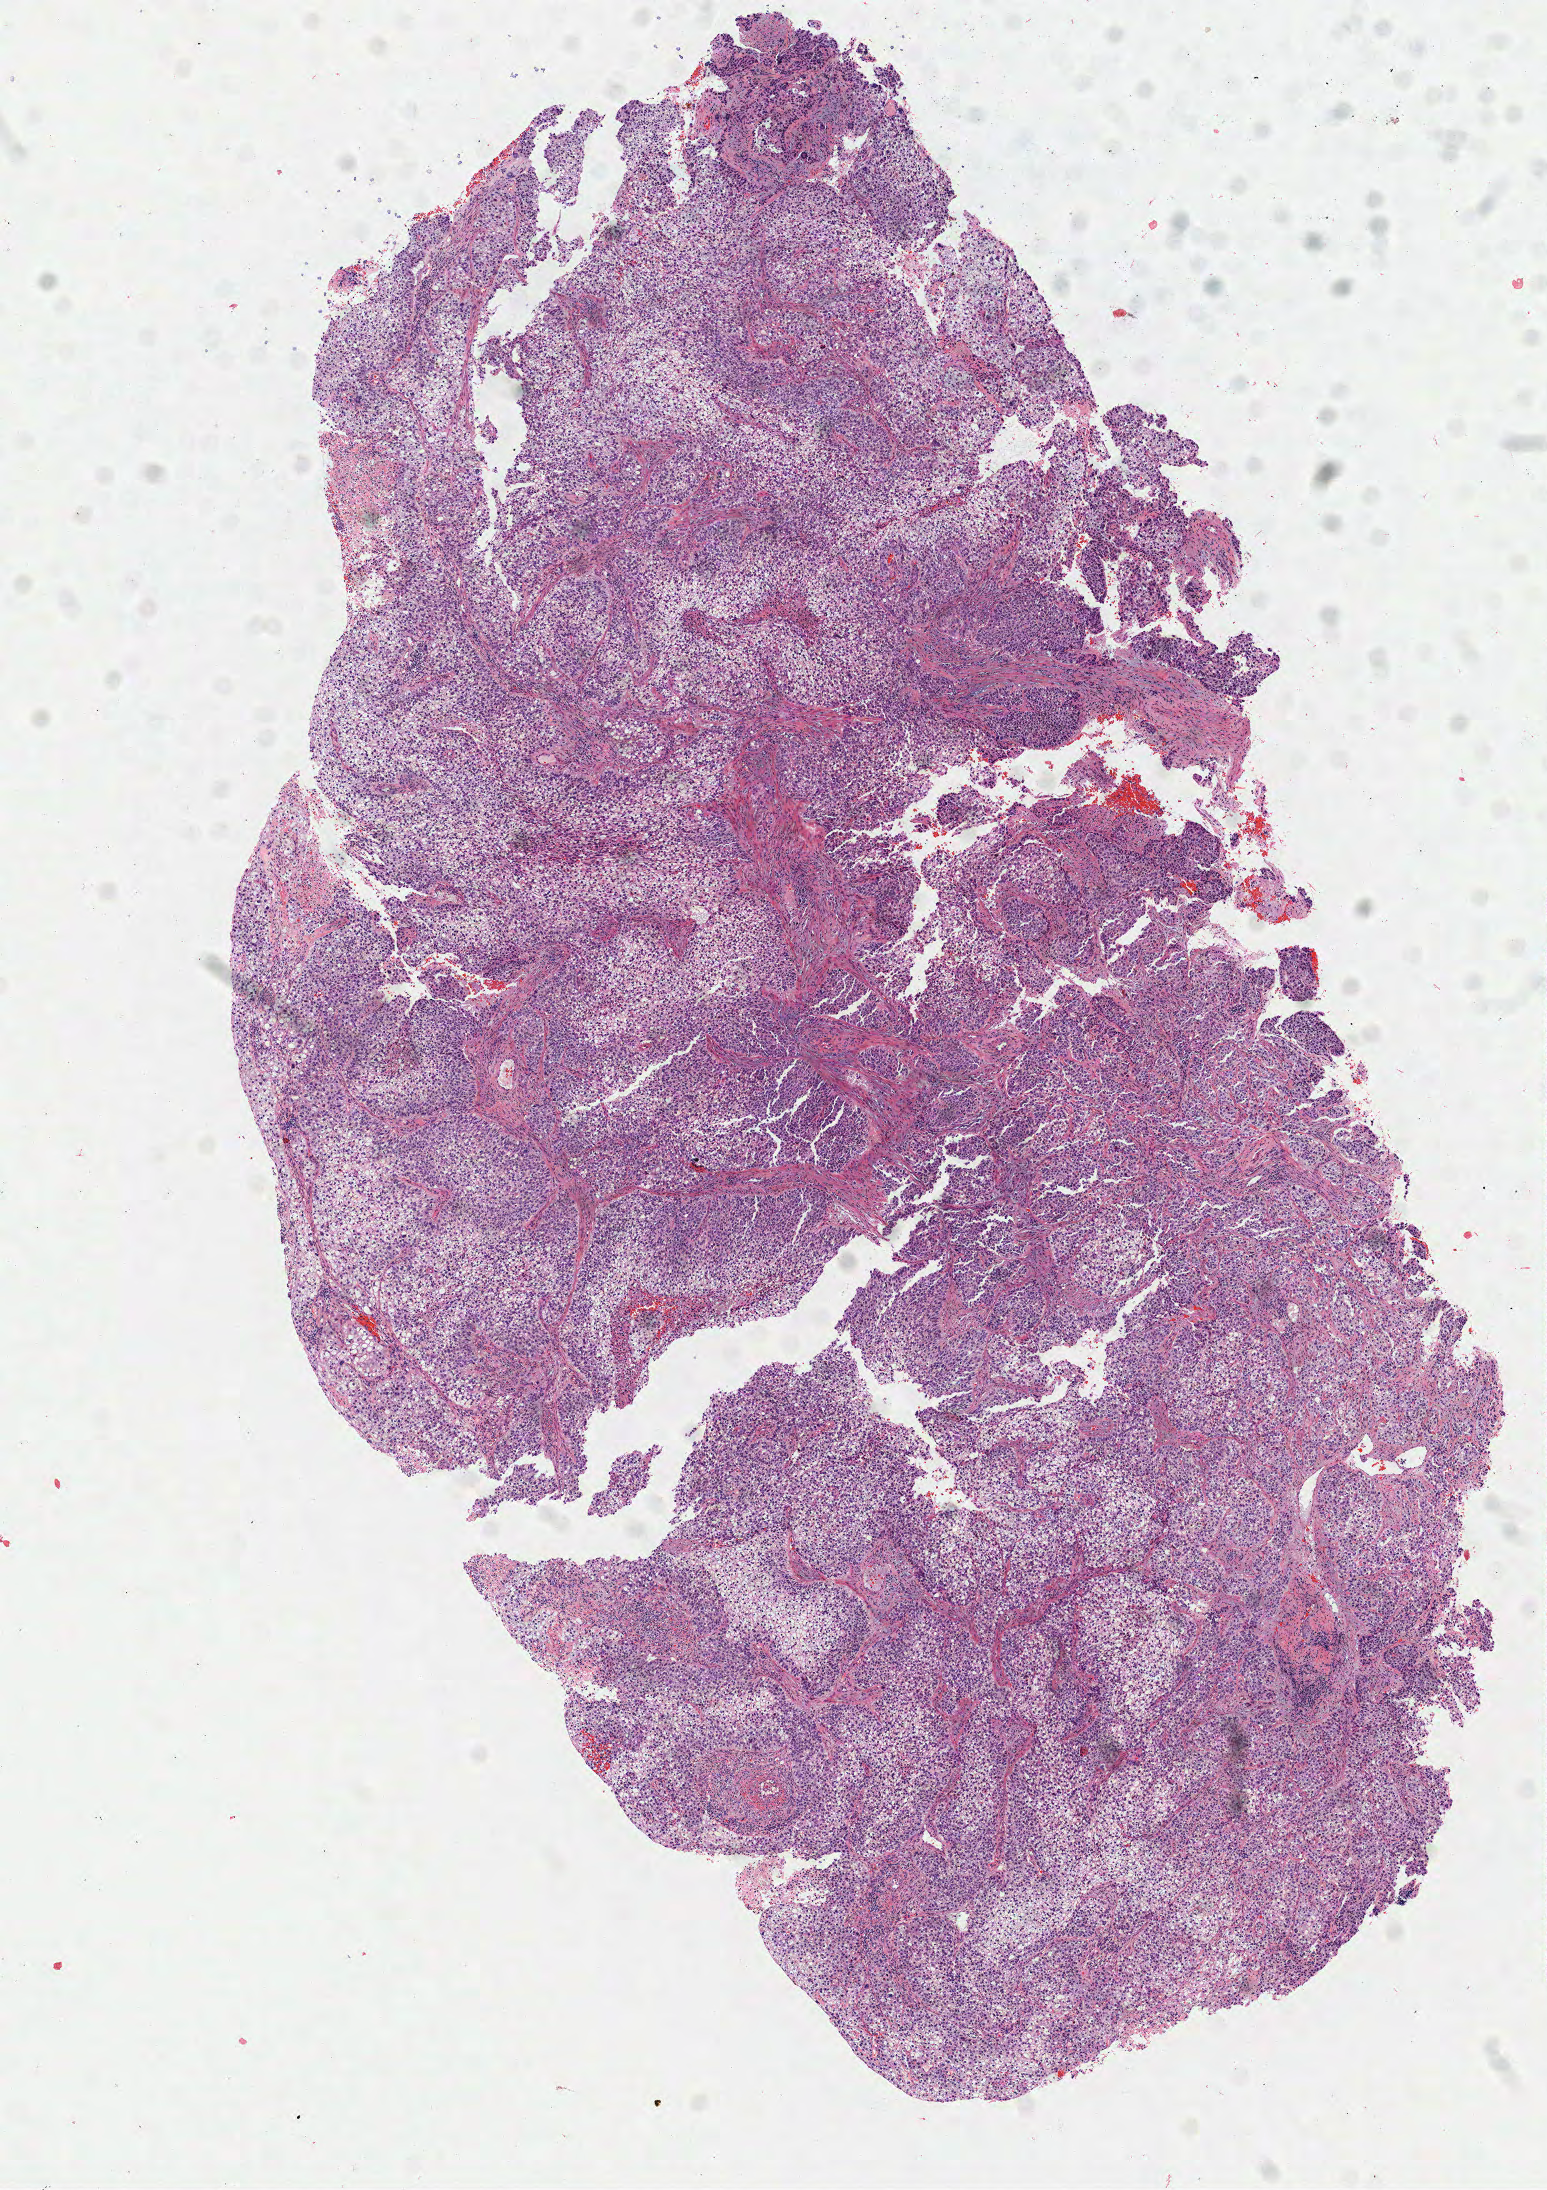
Digitized hematoxylin and eosin (H&E)-stained section, a low-resolution overview of the entire scanned area, about 6.2 x 8.7 mm, specimen: tumor tissue, site: cervix. Female patient, age 39 years.
Histologic diagnosis: Squamous cell carcinoma, large cell, nonkeratinizing, NOS.